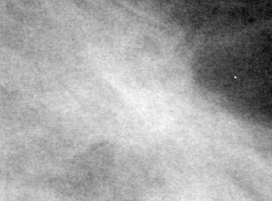
Cropped region of a digitized screen-film mammogram centred on a radiologist-marked abnormality, left breast, MLO view.
- Marked abnormality: mass, shape architectural distortion, margins ill defined / spiculated; BI-RADS assessment category 4; pathology result (as recorded, not read from the image): malignant.